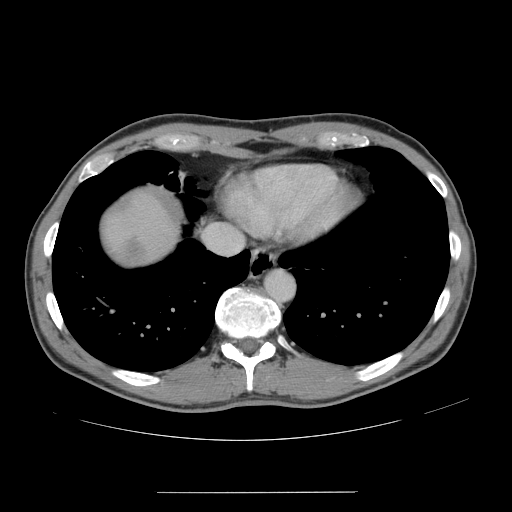
Contrast-enhanced abdominal CT, one axial slice. Slice 142 of 178 in the series (ordered by position). 120 kVp. Intravenous contrast given. Soft-tissue window (W 400 / L 40 HU). 512 × 512 image matrix, field of view 401 × 401 mm. Male patient, age 53 years. From the clinical record (not read from this slice): diagnosis: colorectal cancer liver metastases, imaged before liver resection; multiple liver metastases: yes; largest metastasis: 2.4 cm; disease in both lobes: no.
Structures marked on this image (expert manual segmentation):
- liver: box from (x=102, y=192) to (x=176, y=265) px
- liver metastasis: (x=119, y=236)–(x=146, y=260)